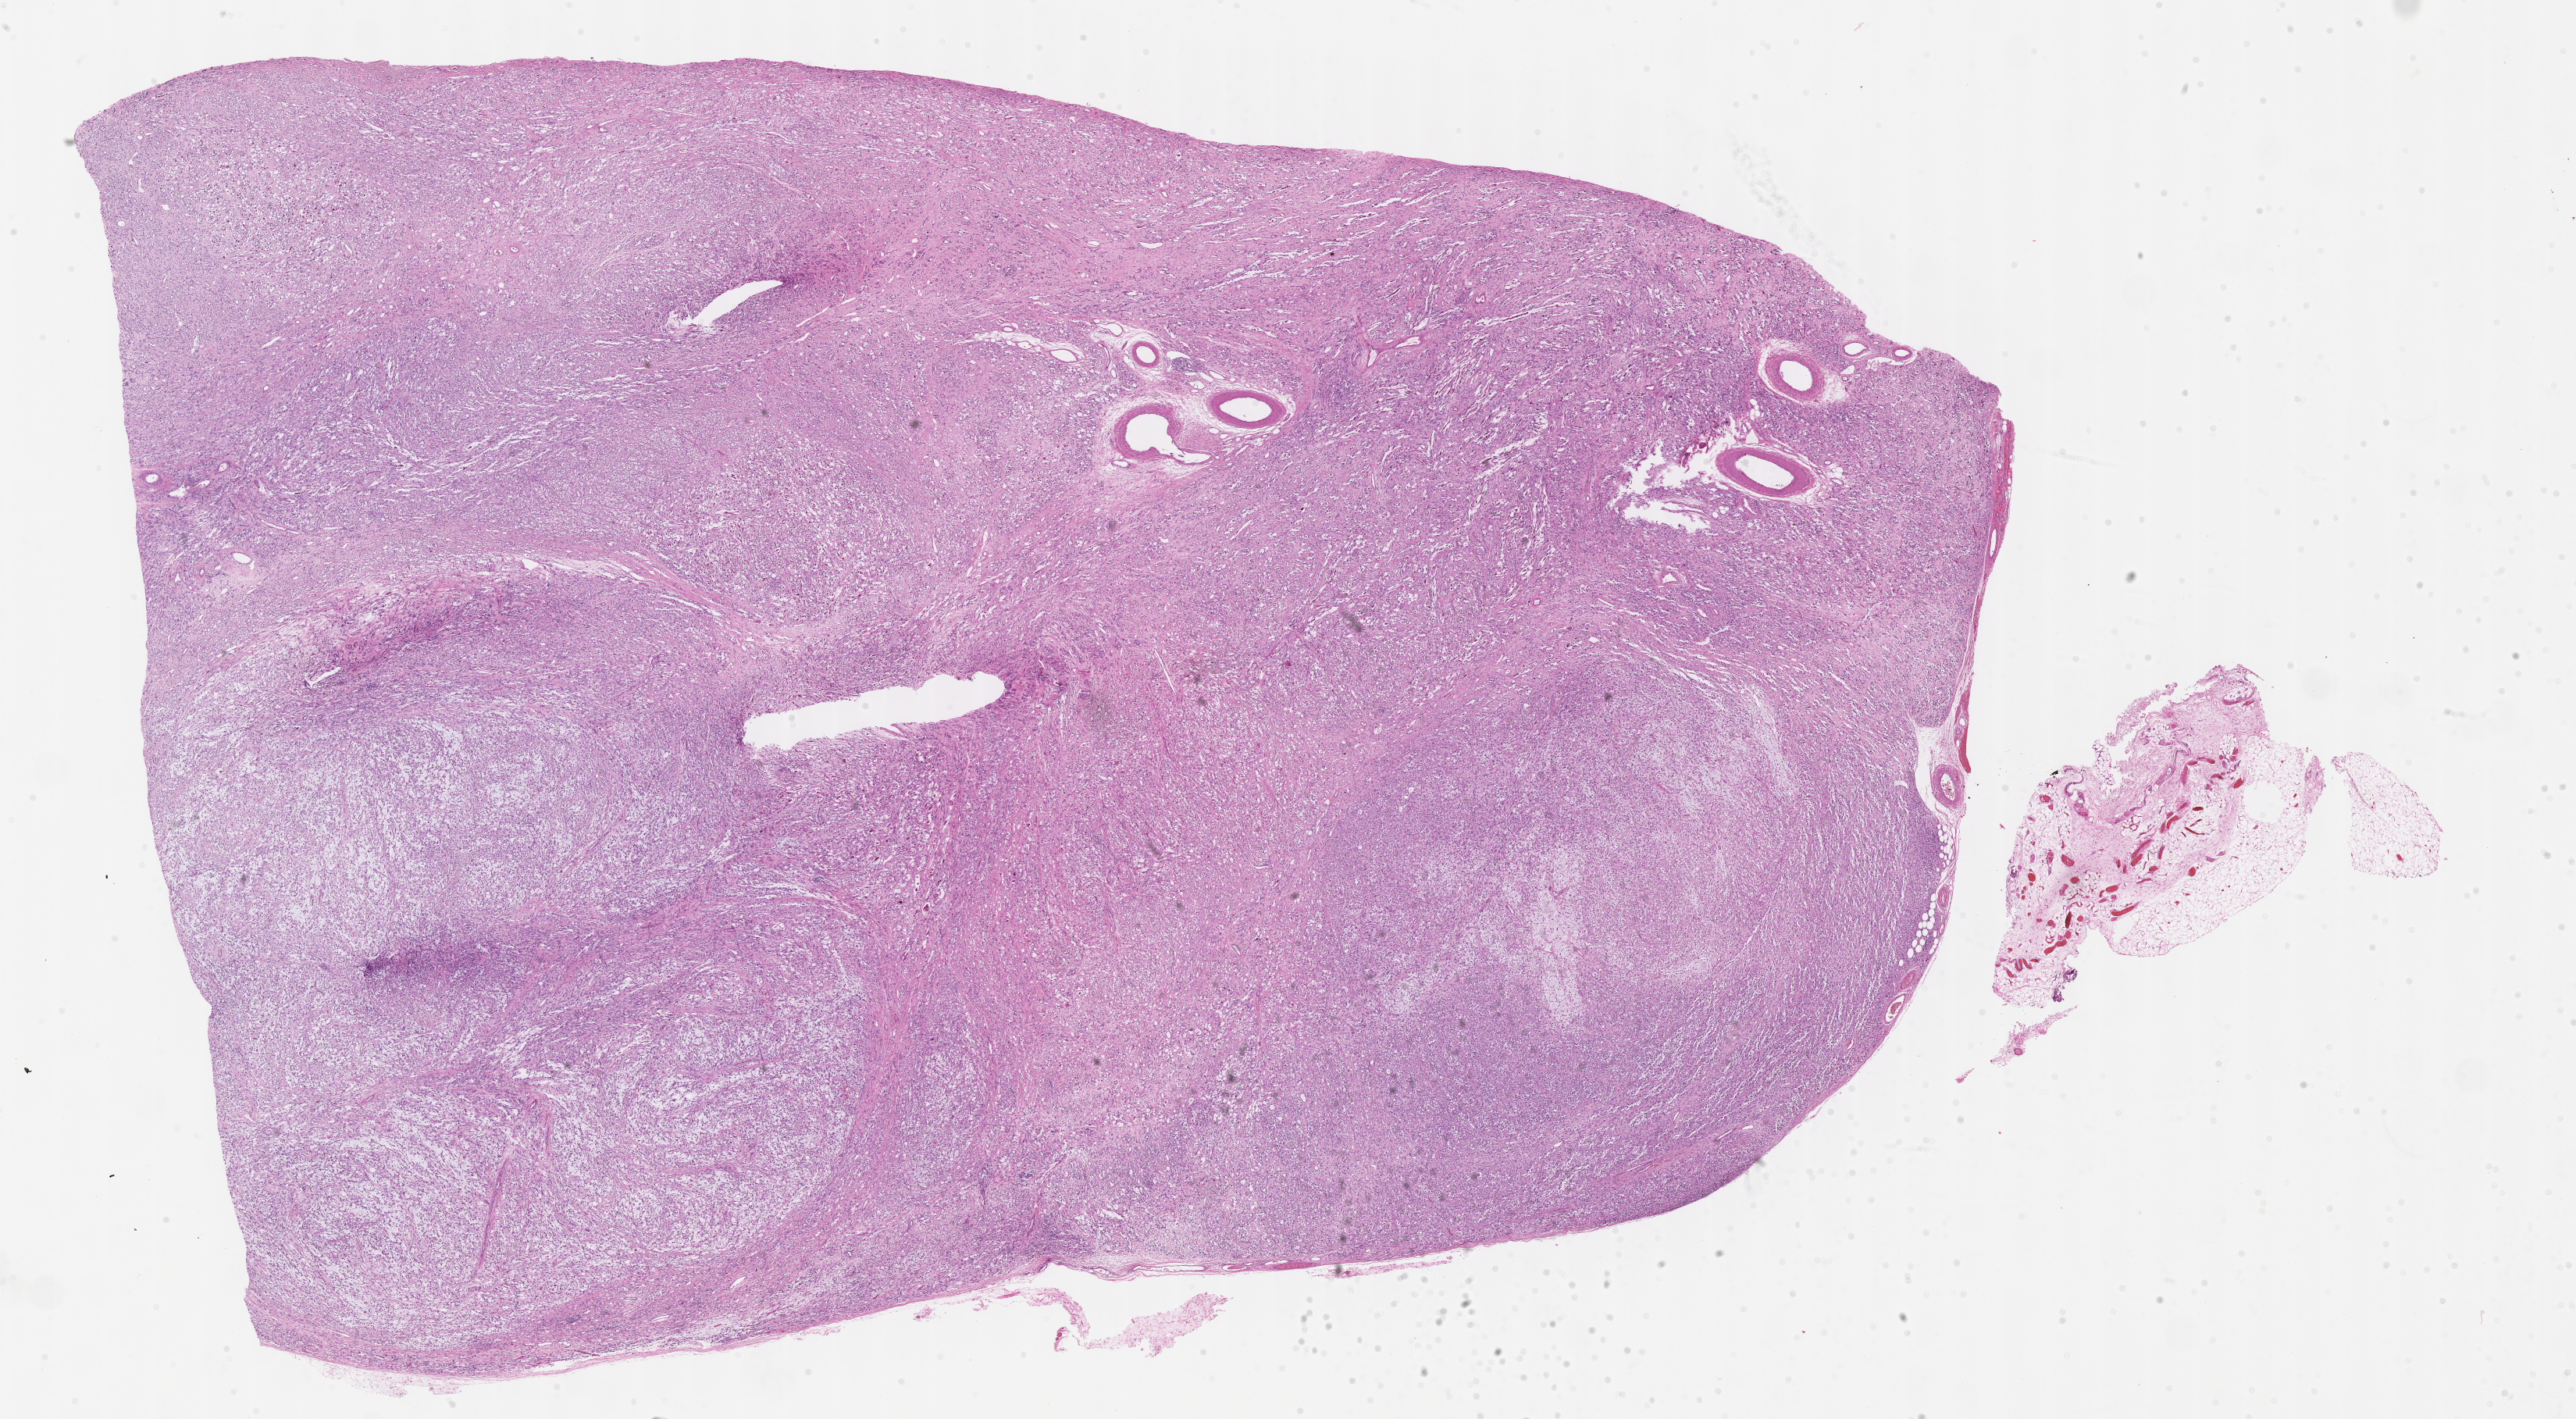
Whole-slide image, H&E stain of tumor tissue, whole scanned area (about 26.7 x 14.7 mm) shown as a low-resolution overview. Formalin-fixed, paraffin-embedded (FFPE) tissue. Site: testicle, right. Male patient, age at diagnosis 1.8 years.
Diagnosis: rhabdomyosarcoma; histological classification: embryonal rhabdomyosarcoma. Stage (as recorded): 1. Primary site (case record): testis-Paratestis. Metastatic status at presentation (as recorded): non-metastatic.